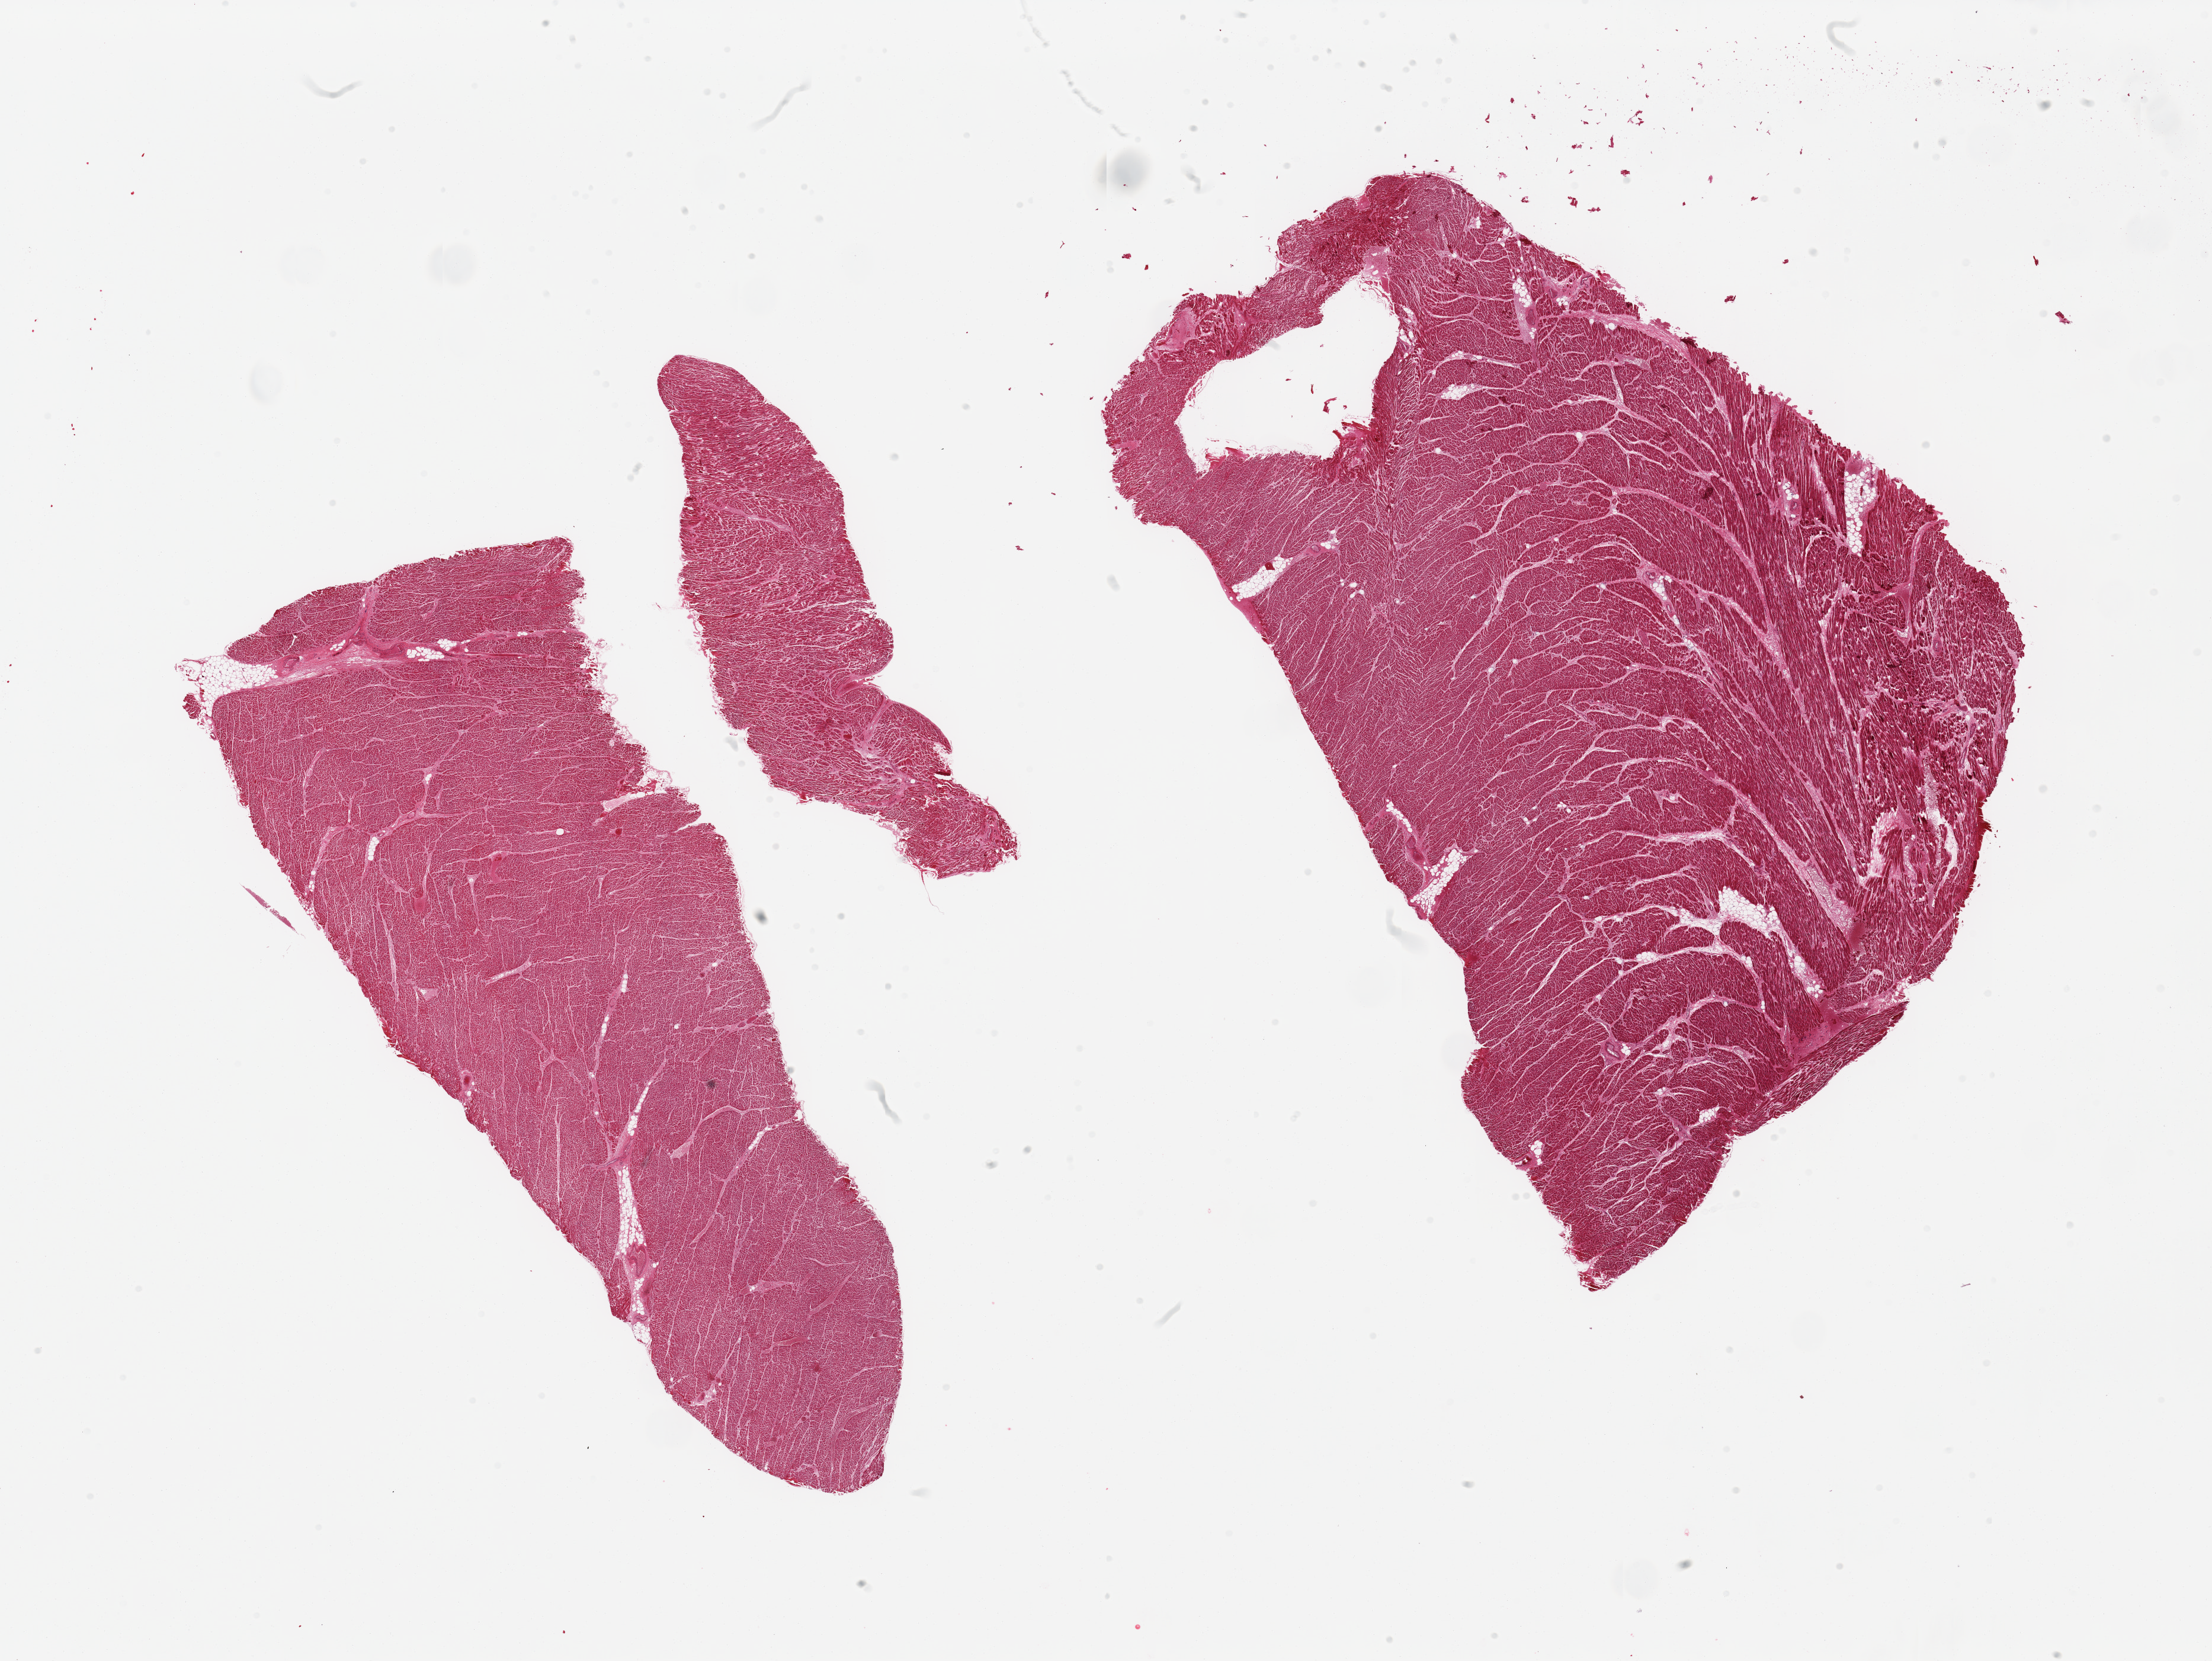
Digitized haematoxylin and eosin-stained section, a low-resolution overview of the entire scanned area, about 29.5 x 22.2 mm (from a 20x scan), PAXgene-fixed paraffin-embedded (PFPE) section, target tissue: heart, donor tissue sample. Male donor.
* review note (as recorded): 2 pieces, minimal interstitial fibrosis